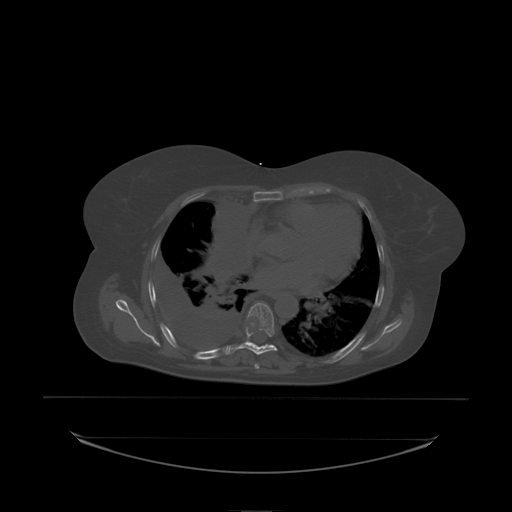
CT including the spine, one axial slice. Position 142 of 242 along the scan axis. Bone window (W 1800 / L 400 HU). 512 × 512 image matrix, field of view 500 × 500 mm. Patient: female, 53 years. Case-level facts recorded for this patient, not image findings: primary cancer: lung; vertebrae with lytic lesions (as recorded): T7, L1.
Annotated regions visible in this slice (semi-automatically segmented with operator editing):
- T7 vertebra: bounding box [x1, y1, x2, y2] px = [246, 303, 275, 338]